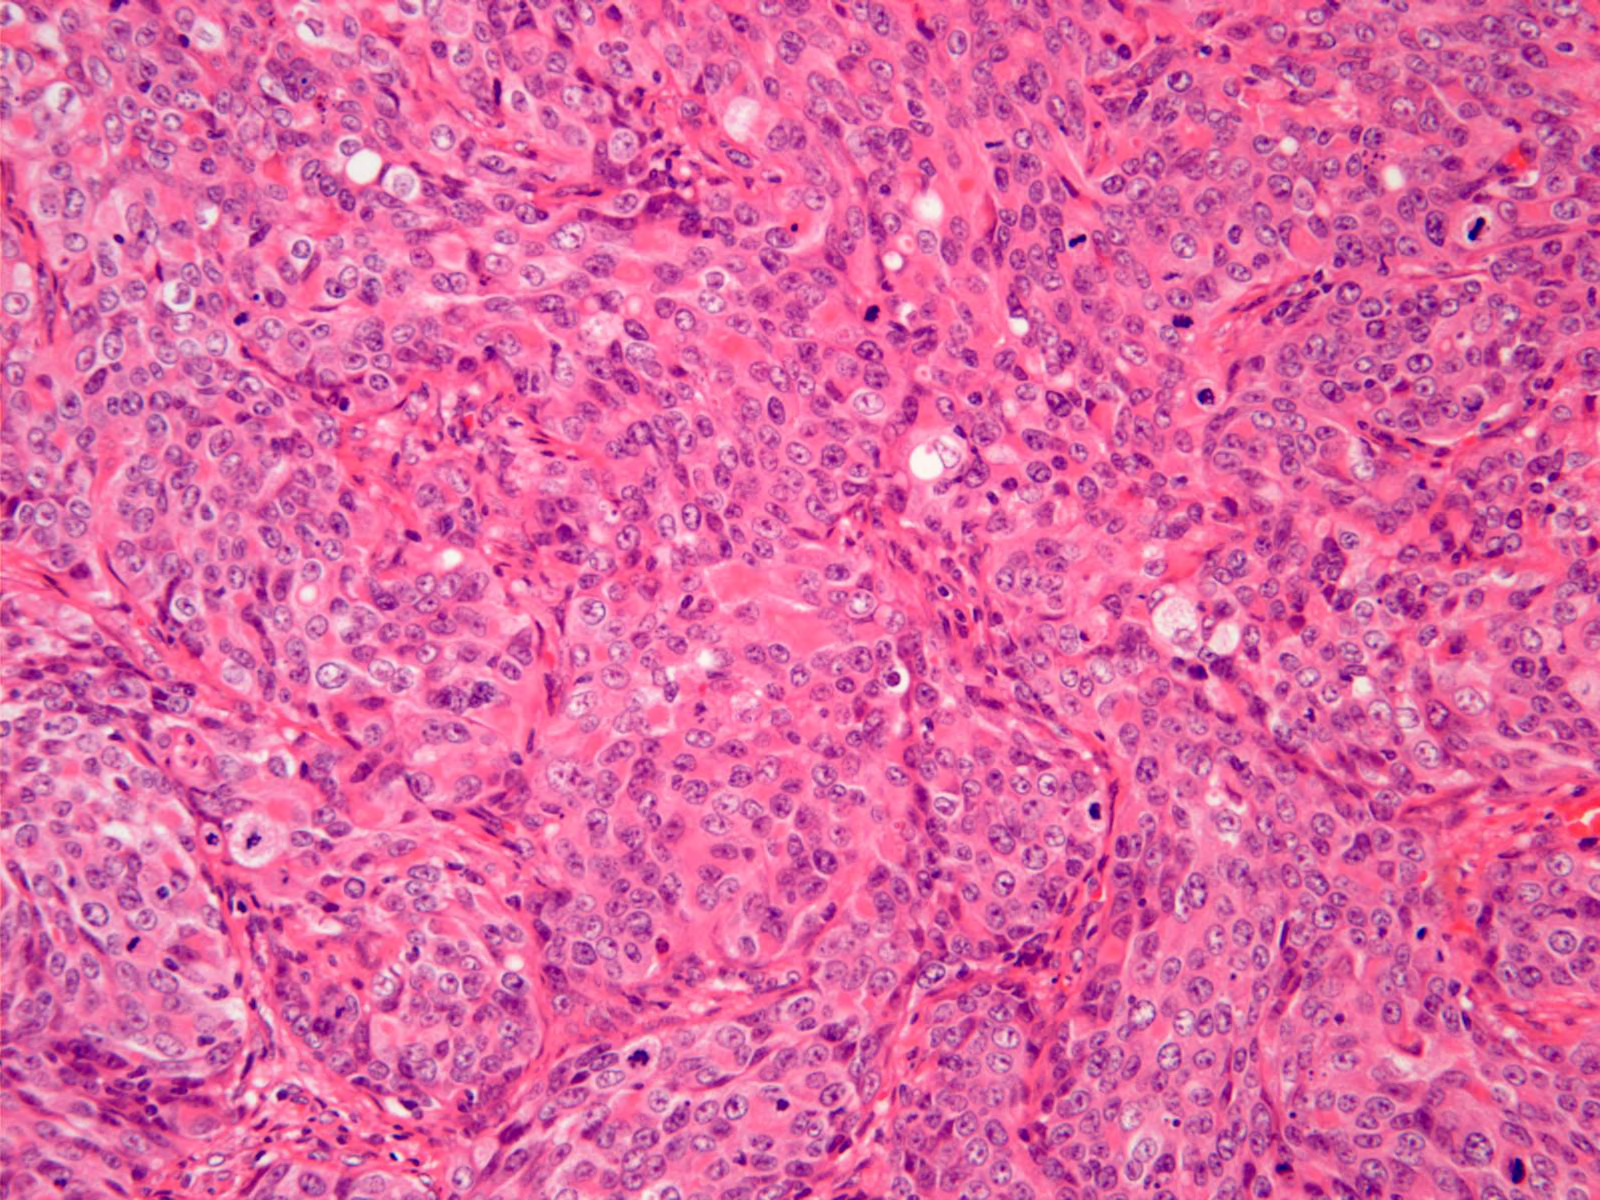
Single-field H&E-stained photomicrograph, about 0.8 x 0.6 mm across, formalin-fixed paraffin-embedded (FFPE) diagnostic section, primary tumour sample from the stomach. Patient: female, age at initial diagnosis 78 years. Histologic grade: G3 (poorly differentiated).
Diagnosis: Adenocarcinoma, NOS (gastric antrum). Lymph nodes positive (case pathology): 8 of 12 examined. AJCC pathologic stage: IV (6th edition).